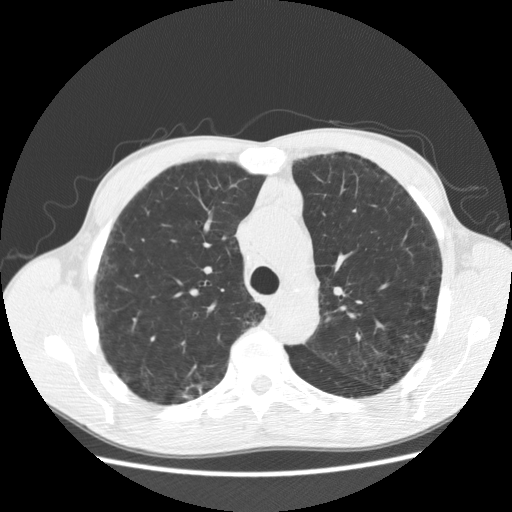
Low-dose screening chest CT, one axial slice. Position 136 of 195 along the scan axis. Reconstruction kernel STANDARD. 120 kVp. Lung window (W 1500 / L -600 HU). 2.5 mm slice thickness. 512 × 512 image matrix.
Outlined on this slice (expert manual segmentation):
- lesion 1 (tumor, upper lobe of right lung): bounding box <184,389,201,398> (left, top, right, bottom; pixels)